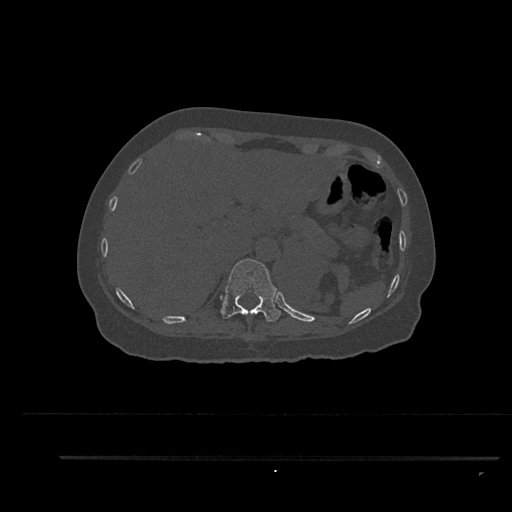
CT including the spine, one axial slice; position 322 of 797 along the scan axis; 120 kVp; bone window (W 1800 / L 400 HU); 512 × 512 image matrix. Female patient, age 44 years. From the clinical record (not read from this slice): primary cancer: renal; vertebrae with lytic lesions (as recorded): L1.
Annotated regions visible in this slice (semi-automatically segmented with operator editing):
- T11 vertebra: bounding box (x1, y1, x2, y2) in pixels: (220, 259, 281, 322)